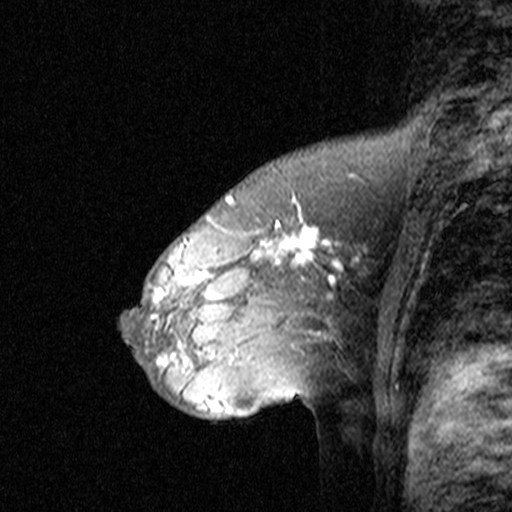
Breast MRI (dynamic contrast-enhanced), one sagittal slice. Position 28 of 44 along the scan axis. Dynamic contrast-enhanced study with each time point stored as its own series, time point 2 of 3 at this slice position (early post-contrast, ordered by acquisition time). 1.5 T. TE 4.5 ms, TR 11 ms. 3 mm slice thickness. 512 × 512 image matrix, field of view 200 × 200 mm. Patient: female, 46 years. Case-level facts recorded for this patient, not image findings: setting: breast cancer imaged before/during neoadjuvant chemotherapy; receptor status: HER2-positive.
Annotated regions visible in this slice (semi-automatically segmented with operator editing):
- analysis volume of interest (the breast-tissue region the enhancement analysis was run in; not a lesion): bounding box <144,172,359,393> (left, top, right, bottom; pixels)
- tumour enhancement mask (voxels above the 90 % enhancement threshold inside the analysis volume of interest): <151,193,343,350>